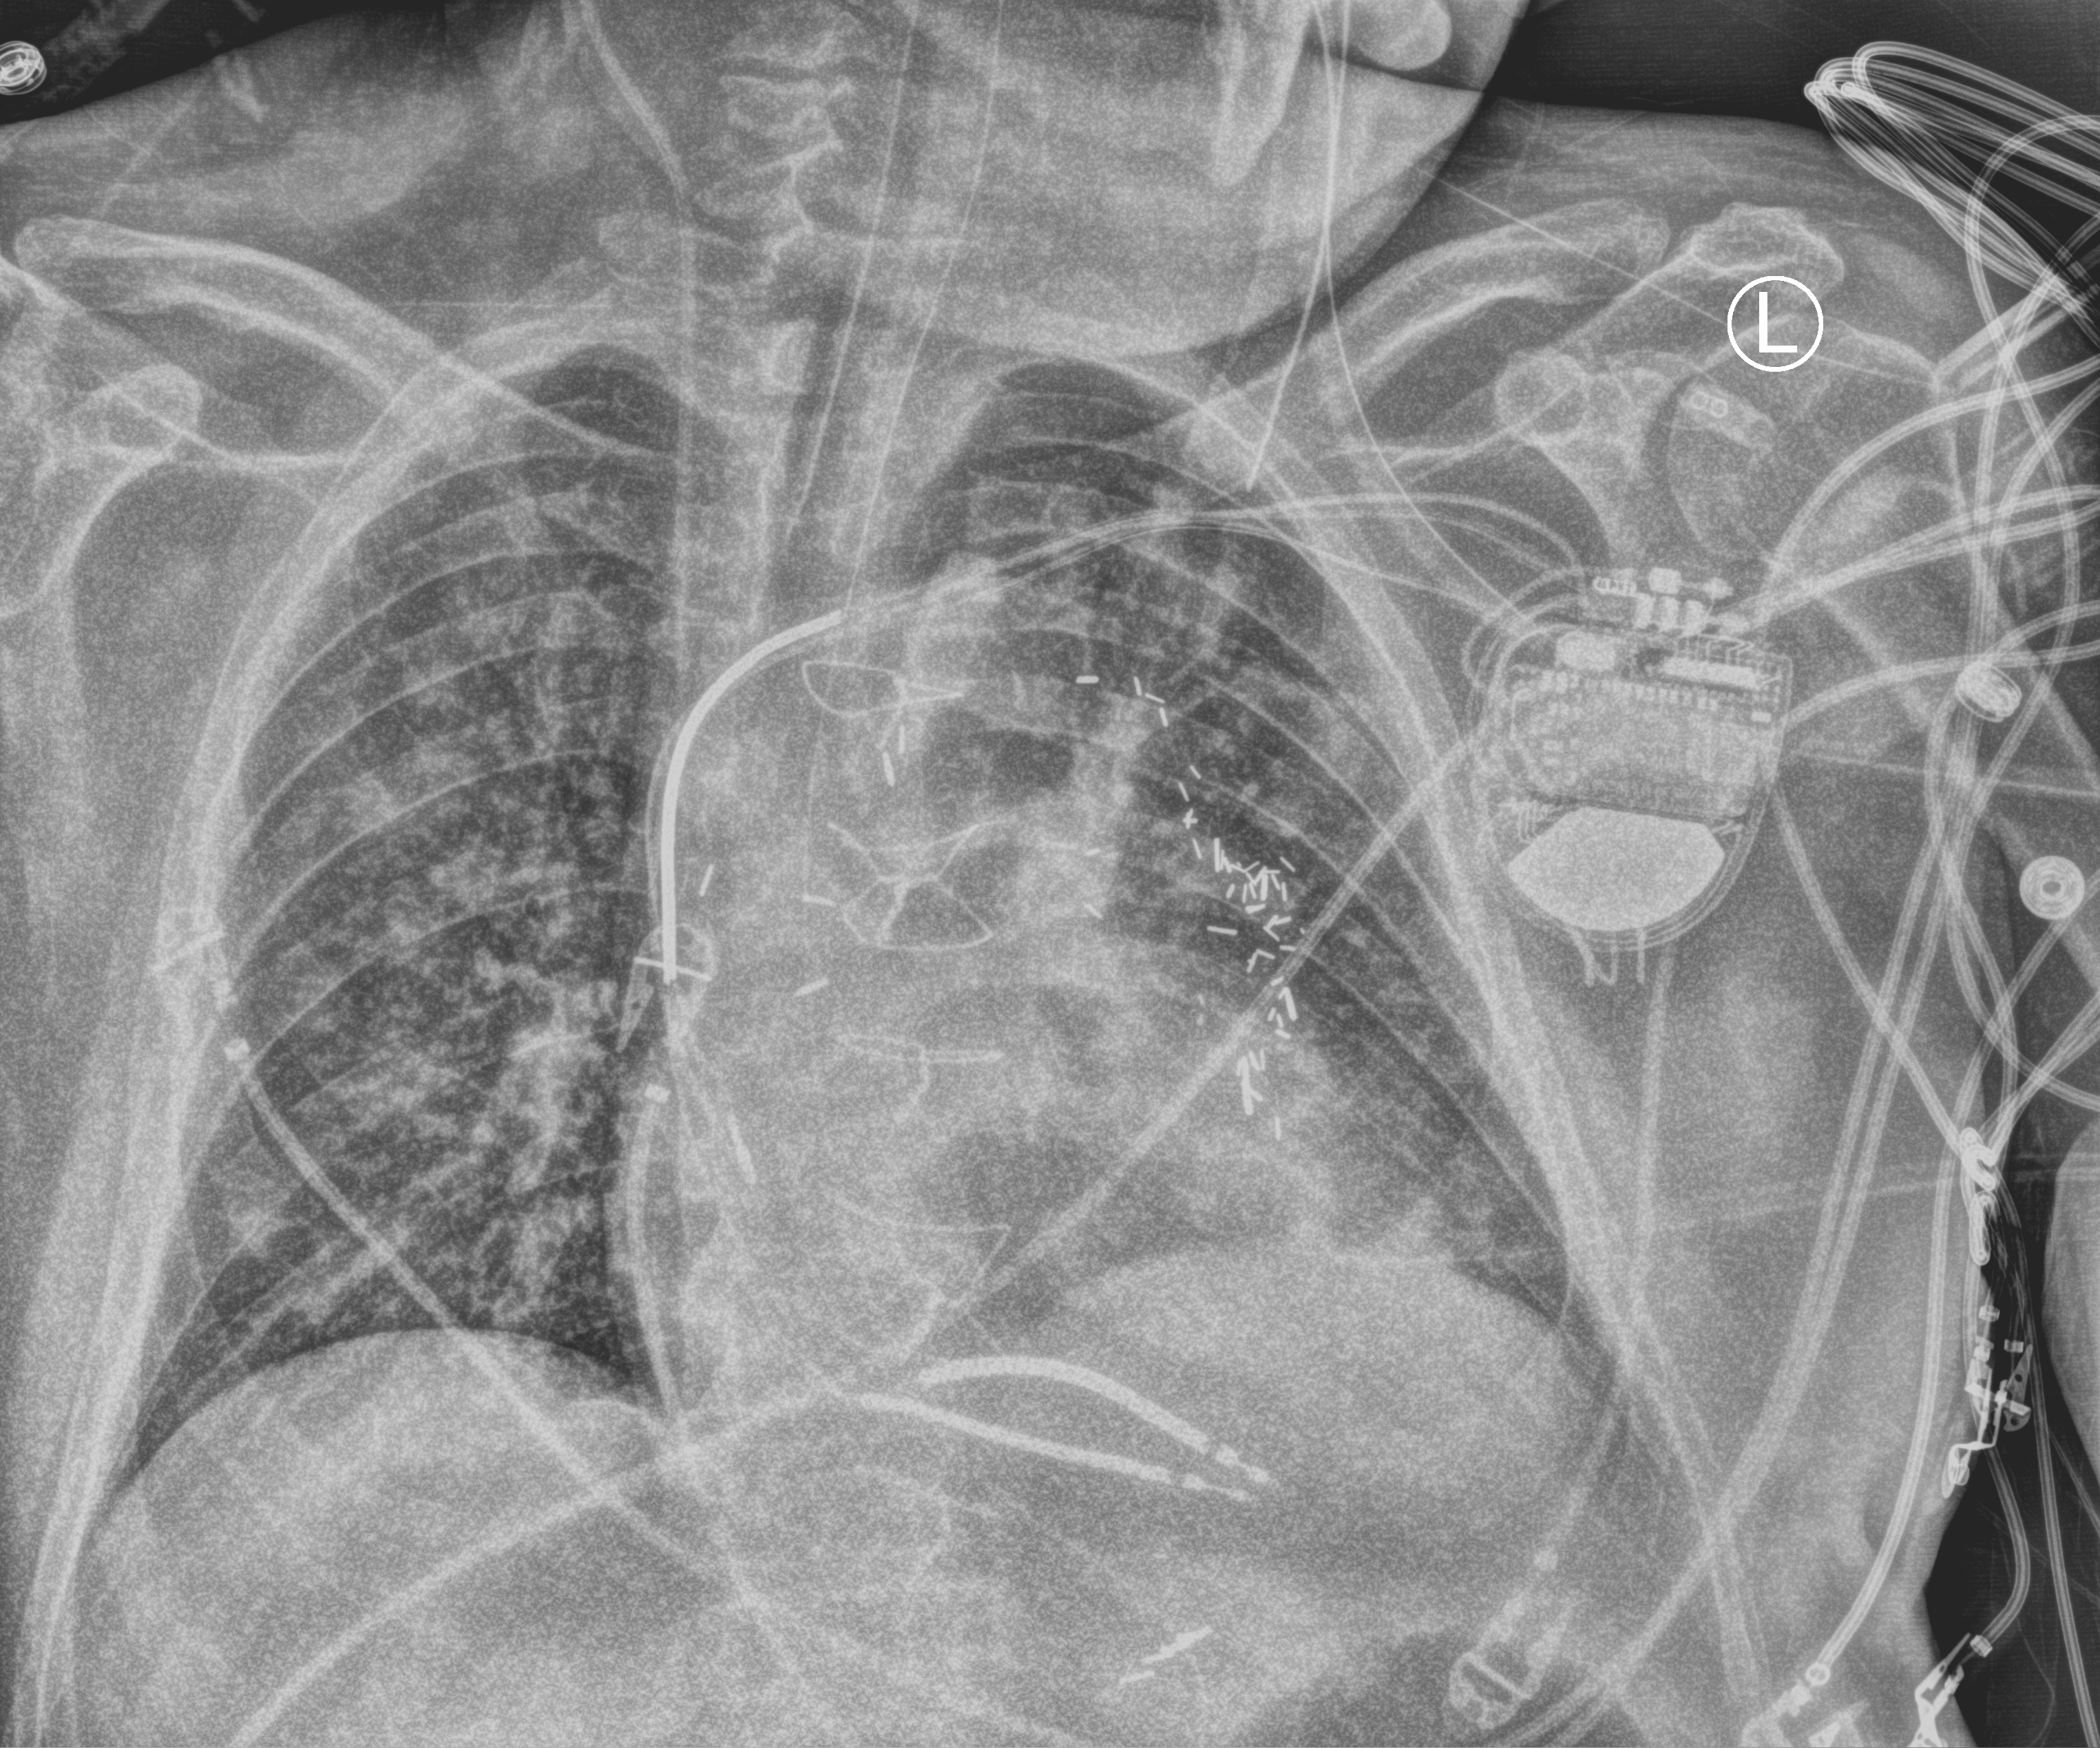
Portable chest radiograph, anteroposterior (AP) projection. Patient hospitalised with COVID-19; male, aged 60–74 years.
Admission-level facts for this patient (not findings on this image; timing relative to this image not recorded):
- other chronic lung disease (admission record): no
- admitted to intensive care during this hospital stay: yes
- mechanically ventilated during this hospital stay: yes